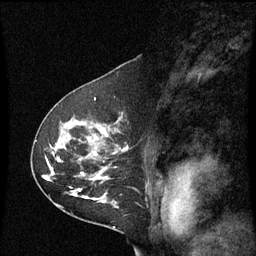
Breast MRI (dynamic contrast-enhanced), one sagittal slice. Position 39 of 60 along the scan axis. Dynamic contrast-enhanced series, image 2 of 3 at this slice position (ordered by acquisition). 1.5 T. TE 4.2 ms, TR 8.9 ms. 2 mm slice thickness. 256 × 256 image matrix, field of view 200 × 200 mm. Patient: female, 53 years. From the clinical record (not read from this slice): setting: breast cancer imaged before/during neoadjuvant chemotherapy; receptor status: HR-positive, HER2-negative.
Structures marked on this image (semi-automatic segmentation, software-assisted and operator-edited):
- analysis volume of interest (the breast-tissue region the enhancement analysis was run in; not a lesion): bounding box [x1, y1, x2, y2] px = [32, 100, 129, 221]
- tumour enhancement mask (voxels above the 70 % enhancement threshold inside the analysis volume of interest): [56, 128, 109, 201]